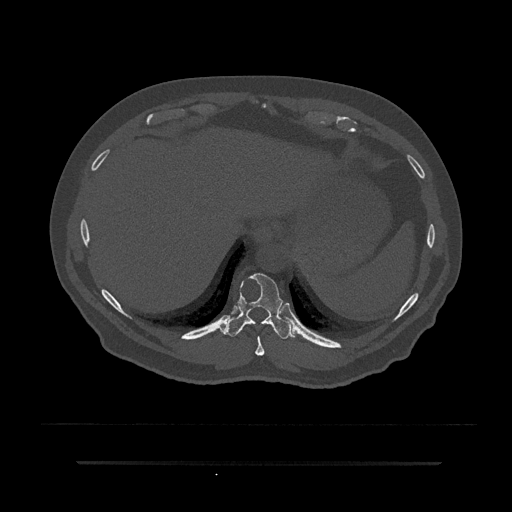
CT including the spine, one axial slice. Position 338 of 797 along the scan axis. Reconstruction kernel Br40s/3. Bone window (W 1800 / L 400 HU). 0.5 mm slice thickness. 512 × 512 image matrix, field of view 464 × 464 mm. Male patient, age 59 years. From the clinical record (not read from this slice): primary cancer: bile ducts; vertebrae with lytic lesions (as recorded): T10.
Annotated regions visible in this slice (semi-automatically segmented with operator editing):
- T10 vertebra: box from (x=224, y=273) to (x=295, y=339) px
- T9 vertebra: (x=255, y=336)–(x=265, y=356)